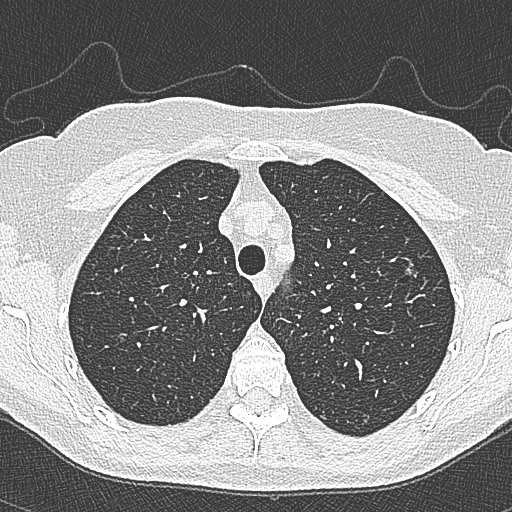
Chest CT (low-dose screening protocol), one axial image, second annual screen, lung window (W 1500 / L -600 HU), 1 mm slice thickness, 120 kVp, slice 74 of 350 in the series, 512 × 512 image matrix. Female, age 65 years at enrolment. Current smoker at enrolment.
- Expert reader's lesion annotation, bounding box [x1, y1, x2, y2] px = [393, 251, 432, 291].
- The screening reader recorded 4 non-calcified nodules or masses ≥4 mm on this exam (left upper lobe, left upper lobe, left upper lobe, right lower lobe); which of them this box marks is not recorded.
- Official screen result: positive, change unspecified: nodule(s) >= 4 mm or enlarging nodule(s), mass(es), or other non-specific abnormalities suspicious for lung cancer.